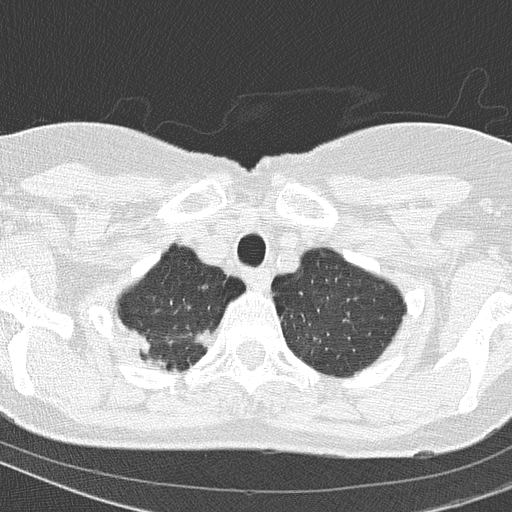
Low-dose screening chest CT, one axial slice. Position 138 of 154 along the scan axis. 120 kVp. Lung window (W 1500 / L -600 HU). 2 mm slice thickness. 512 × 512 image matrix, field of view 288 × 288 mm.
Annotated regions visible in this slice (outlined manually by an expert reader):
- lesion 1 (tumor, upper lobe of right lung): box from (x=146, y=358) to (x=179, y=373) px